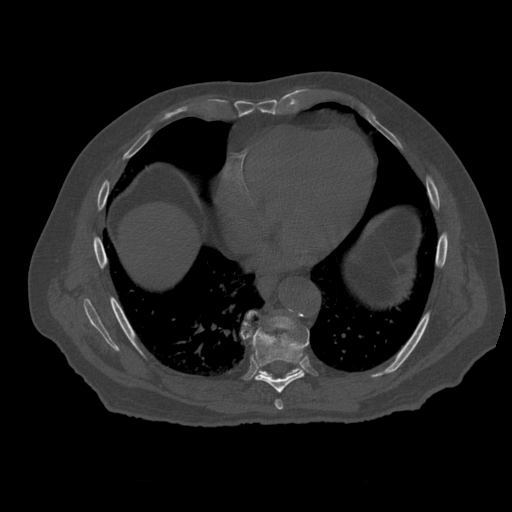
CT including the spine, one axial slice. Position 336 of 399 along the scan axis. Bone window (W 1800 / L 400 HU). 1.25 mm slice thickness. 512 × 512 image matrix, field of view 407 × 407 mm. Patient age 73 years. From the clinical record (not read from this slice): primary cancer: prostate.
Annotated regions visible in this slice (semi-automatically segmented with operator editing):
- T7 vertebra: bounding box (x1, y1, x2, y2) in pixels: (275, 400, 283, 410)
- T8 vertebra: (244, 322, 309, 393)
- T9 vertebra: (242, 311, 302, 379)